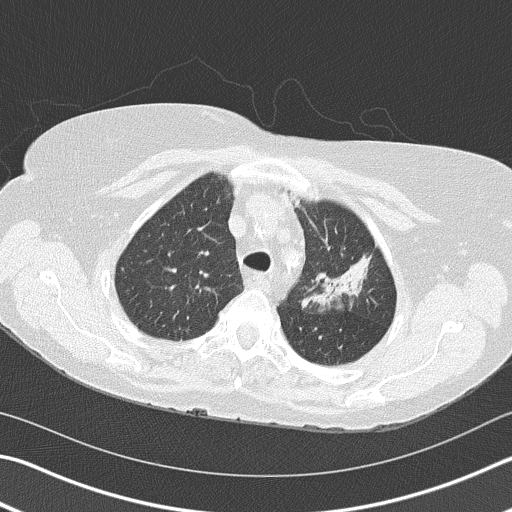
Low-dose screening chest CT, axial slice. Second annual screen. Lung window (W 1500 / L -600 HU). 2 mm slice thickness. Female participant, aged 68 years at enrolment. Former smoker at enrolment.
Expert-annotated lung lesion, box from (x=291, y=221) to (x=380, y=320) px. The exam's reader record, not a measurement of the box and not confirmed to be the same lesion: non-calcified nodule or mass ≥4 mm, left upper lobe, 4 × 2 mm, spiculated (stellate) margins, soft tissue attenuation, pre-existing on the prior screen: yes; interval growth: yes. Official screen result: positive, other. Later outcome: lung cancer diagnosed 392 days after this screen — adenocarcinoma, NOS, left upper lobe, poorly differentiated (G3), stage IB (AJCC 6th edition), 50 mm at pathology.